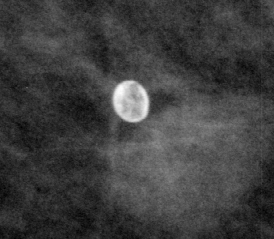
Region of interest cut from a scanned film mammogram (one marked finding); left breast; CC view.
- Marked abnormality: mass, shape oval, margins microlobulated; BI-RADS assessment category 4; subtlety rating 5 on a 1 (subtle) to 5 (obvious) scale; pathology result (as recorded, not read from the image): malignant.